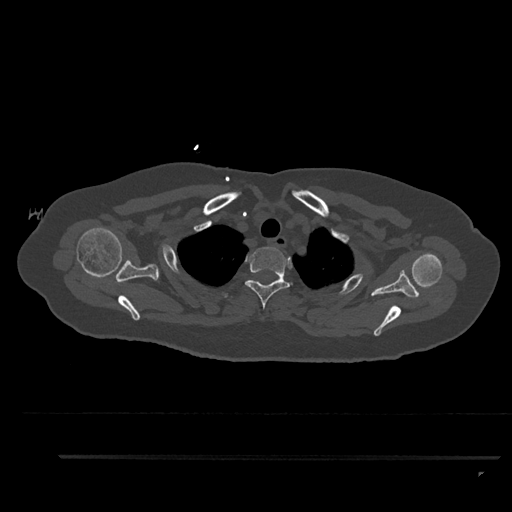
CT including the spine, one axial slice. Position 721 of 797 along the scan axis. 120 kVp. Bone window (W 1800 / L 400 HU). 512 × 512 image matrix, field of view 408 × 408 mm. Patient: female, 44 years. Case-level facts recorded for this patient, not image findings: primary cancer: renal.
Annotated regions visible in this slice (semi-automatically segmented with operator editing):
- T2 vertebra: bounding box (x1, y1, x2, y2) in pixels: (245, 247, 293, 309)